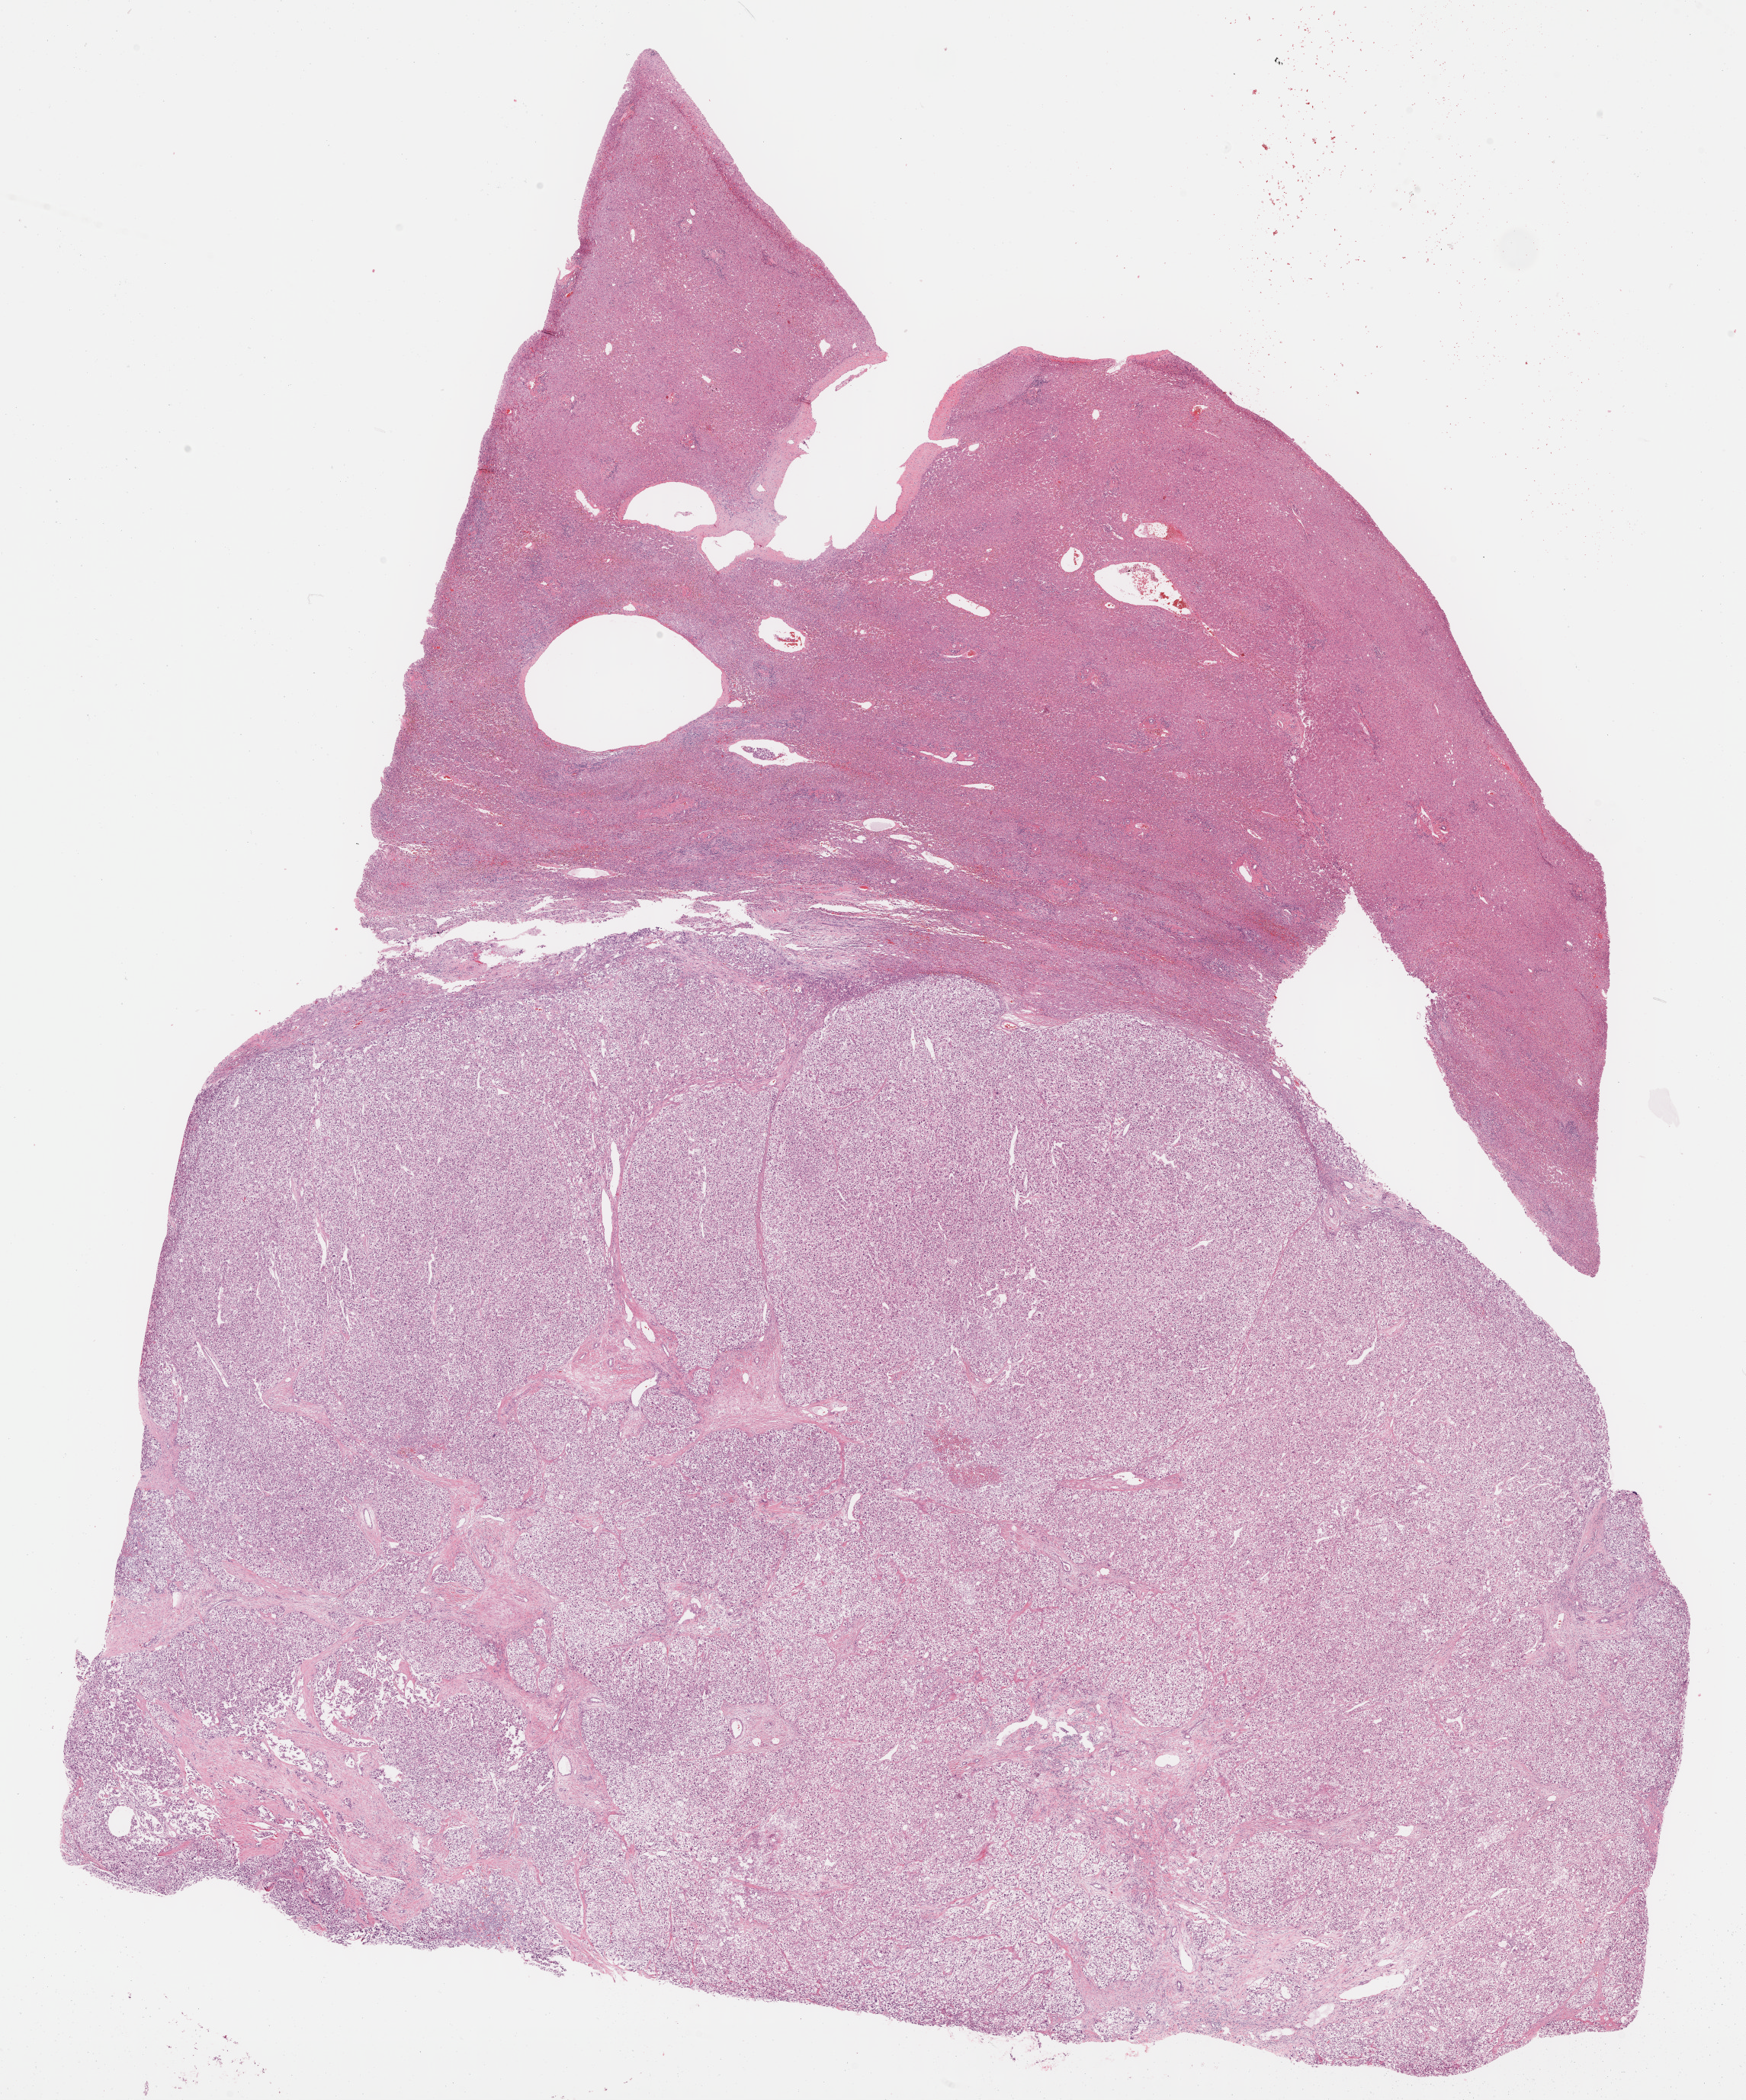
Whole-slide histology image, H&E — low-resolution overview of the scanned area, about 18.5 x 22.3 mm (slide scanned at 40x), FFPE section, liver, primary tumour sample. Female patient; age at initial diagnosis 64 years. Histologic grade: G2 (moderately differentiated).
AJCC pathologic stage: IVB. Histologic diagnosis: Hepatocellular carcinoma, NOS. TNM: T4 N0 M1.